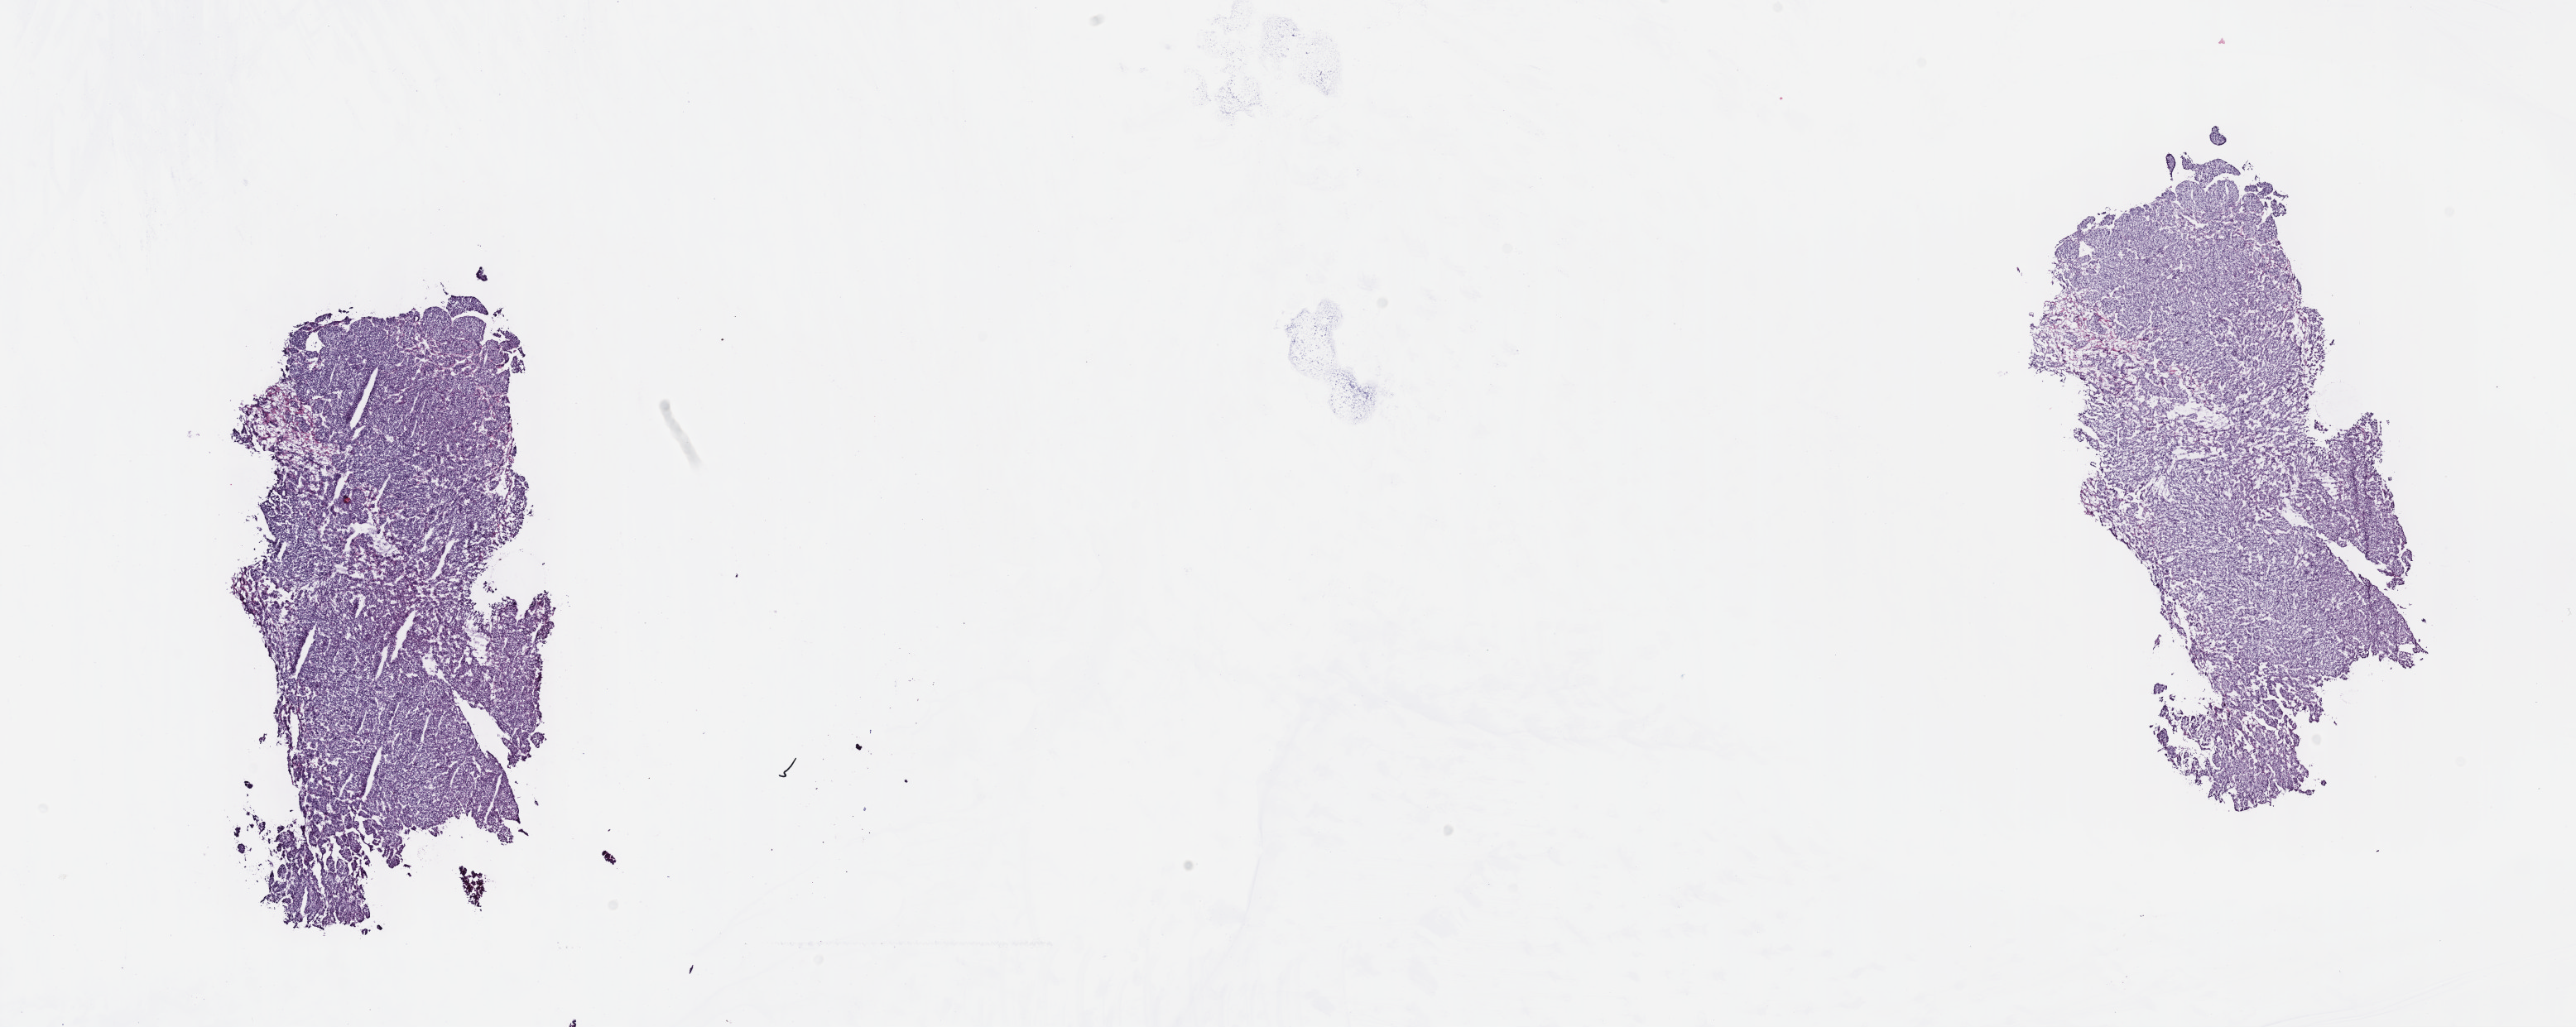
Whole-slide histology image, Hematoxylin and eosin (H&E) stained — low-resolution overview of the scanned area, about 25.2 x 10.0 mm; frozen section from the top of the tissue portion; primary tumour sample from the liver. Patient: male, age at initial diagnosis 18 years. Histologic grade: G1 (well differentiated). Slide review estimates, as recorded: tumour cells 100%, tumour nuclei 95%, normal cells 0%, stromal cells 0%, necrosis 0%. Infiltration values recorded for this section: lymphocyte infiltration 0%, monocyte infiltration 0%, neutrophil infiltration 0%.
* AJCC pathologic stage: IIIC (6th edition)
* diagnosis: Hepatocellular carcinoma, NOS